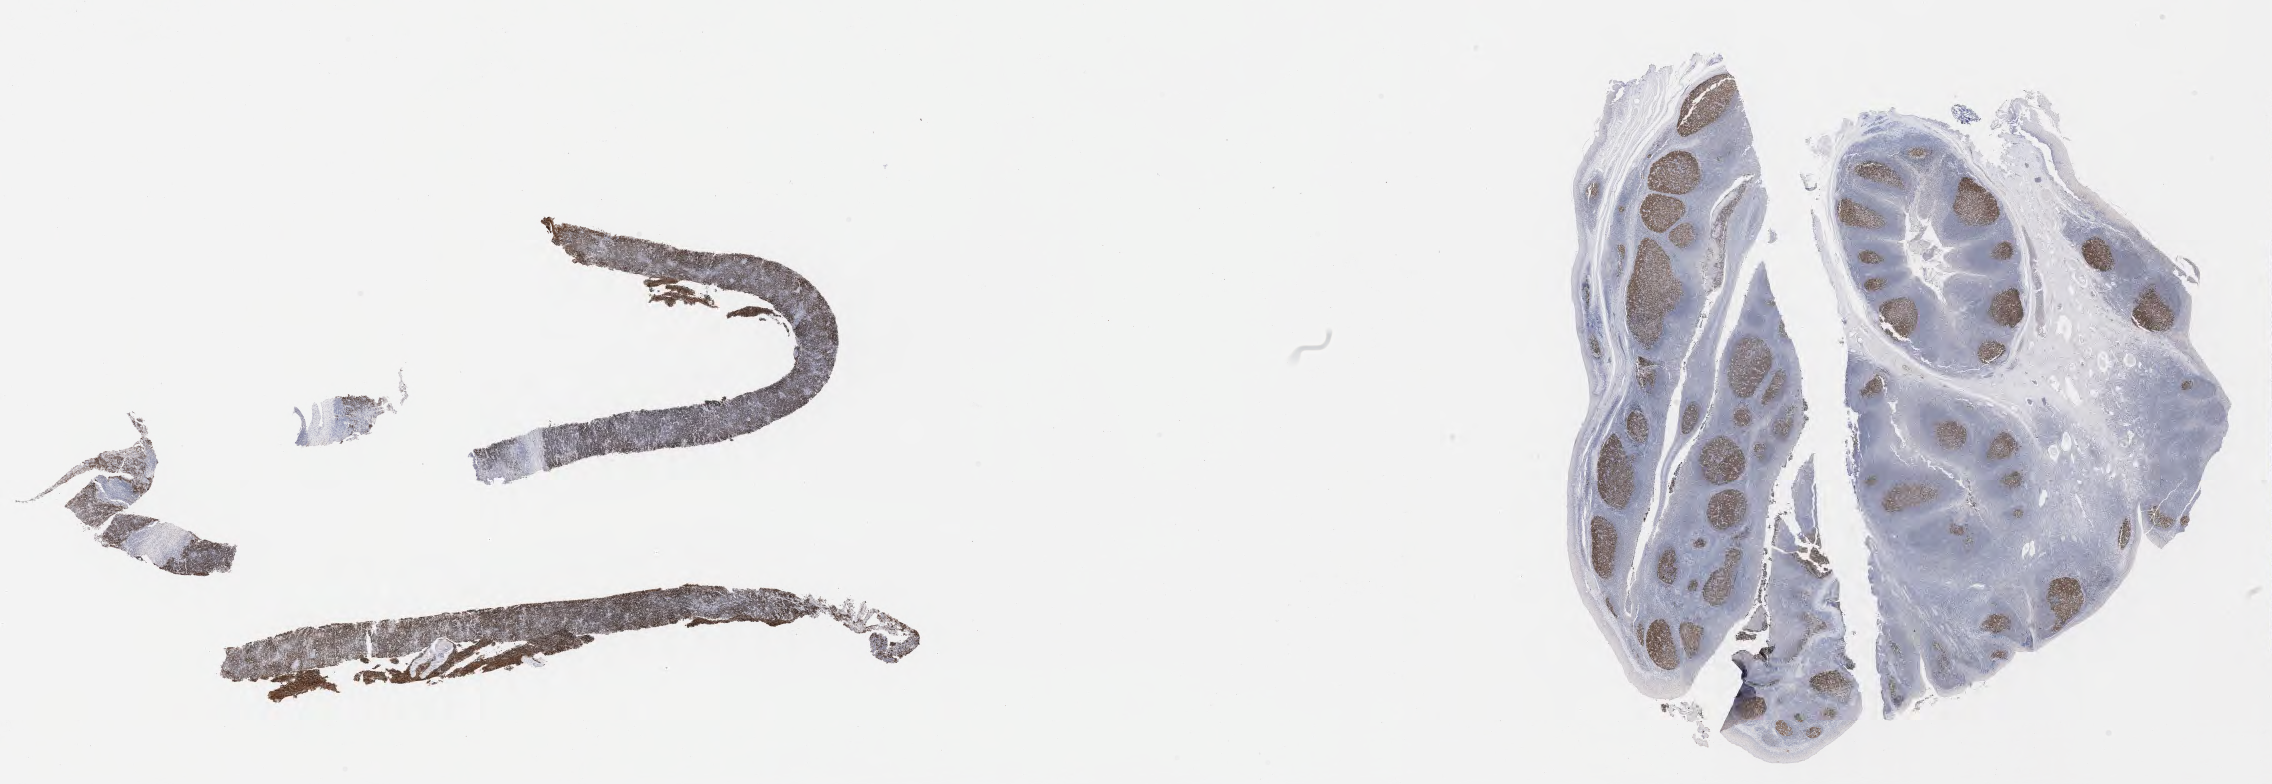
Whole-slide image, immunohistochemical stain for BCL6, whole scanned area (about 36.7 x 12.7 mm) shown as a low-resolution overview; specimen: tumor tissue. Male patient, 55 years old.
Diagnosis: Burkitt lymphoma, NOS.